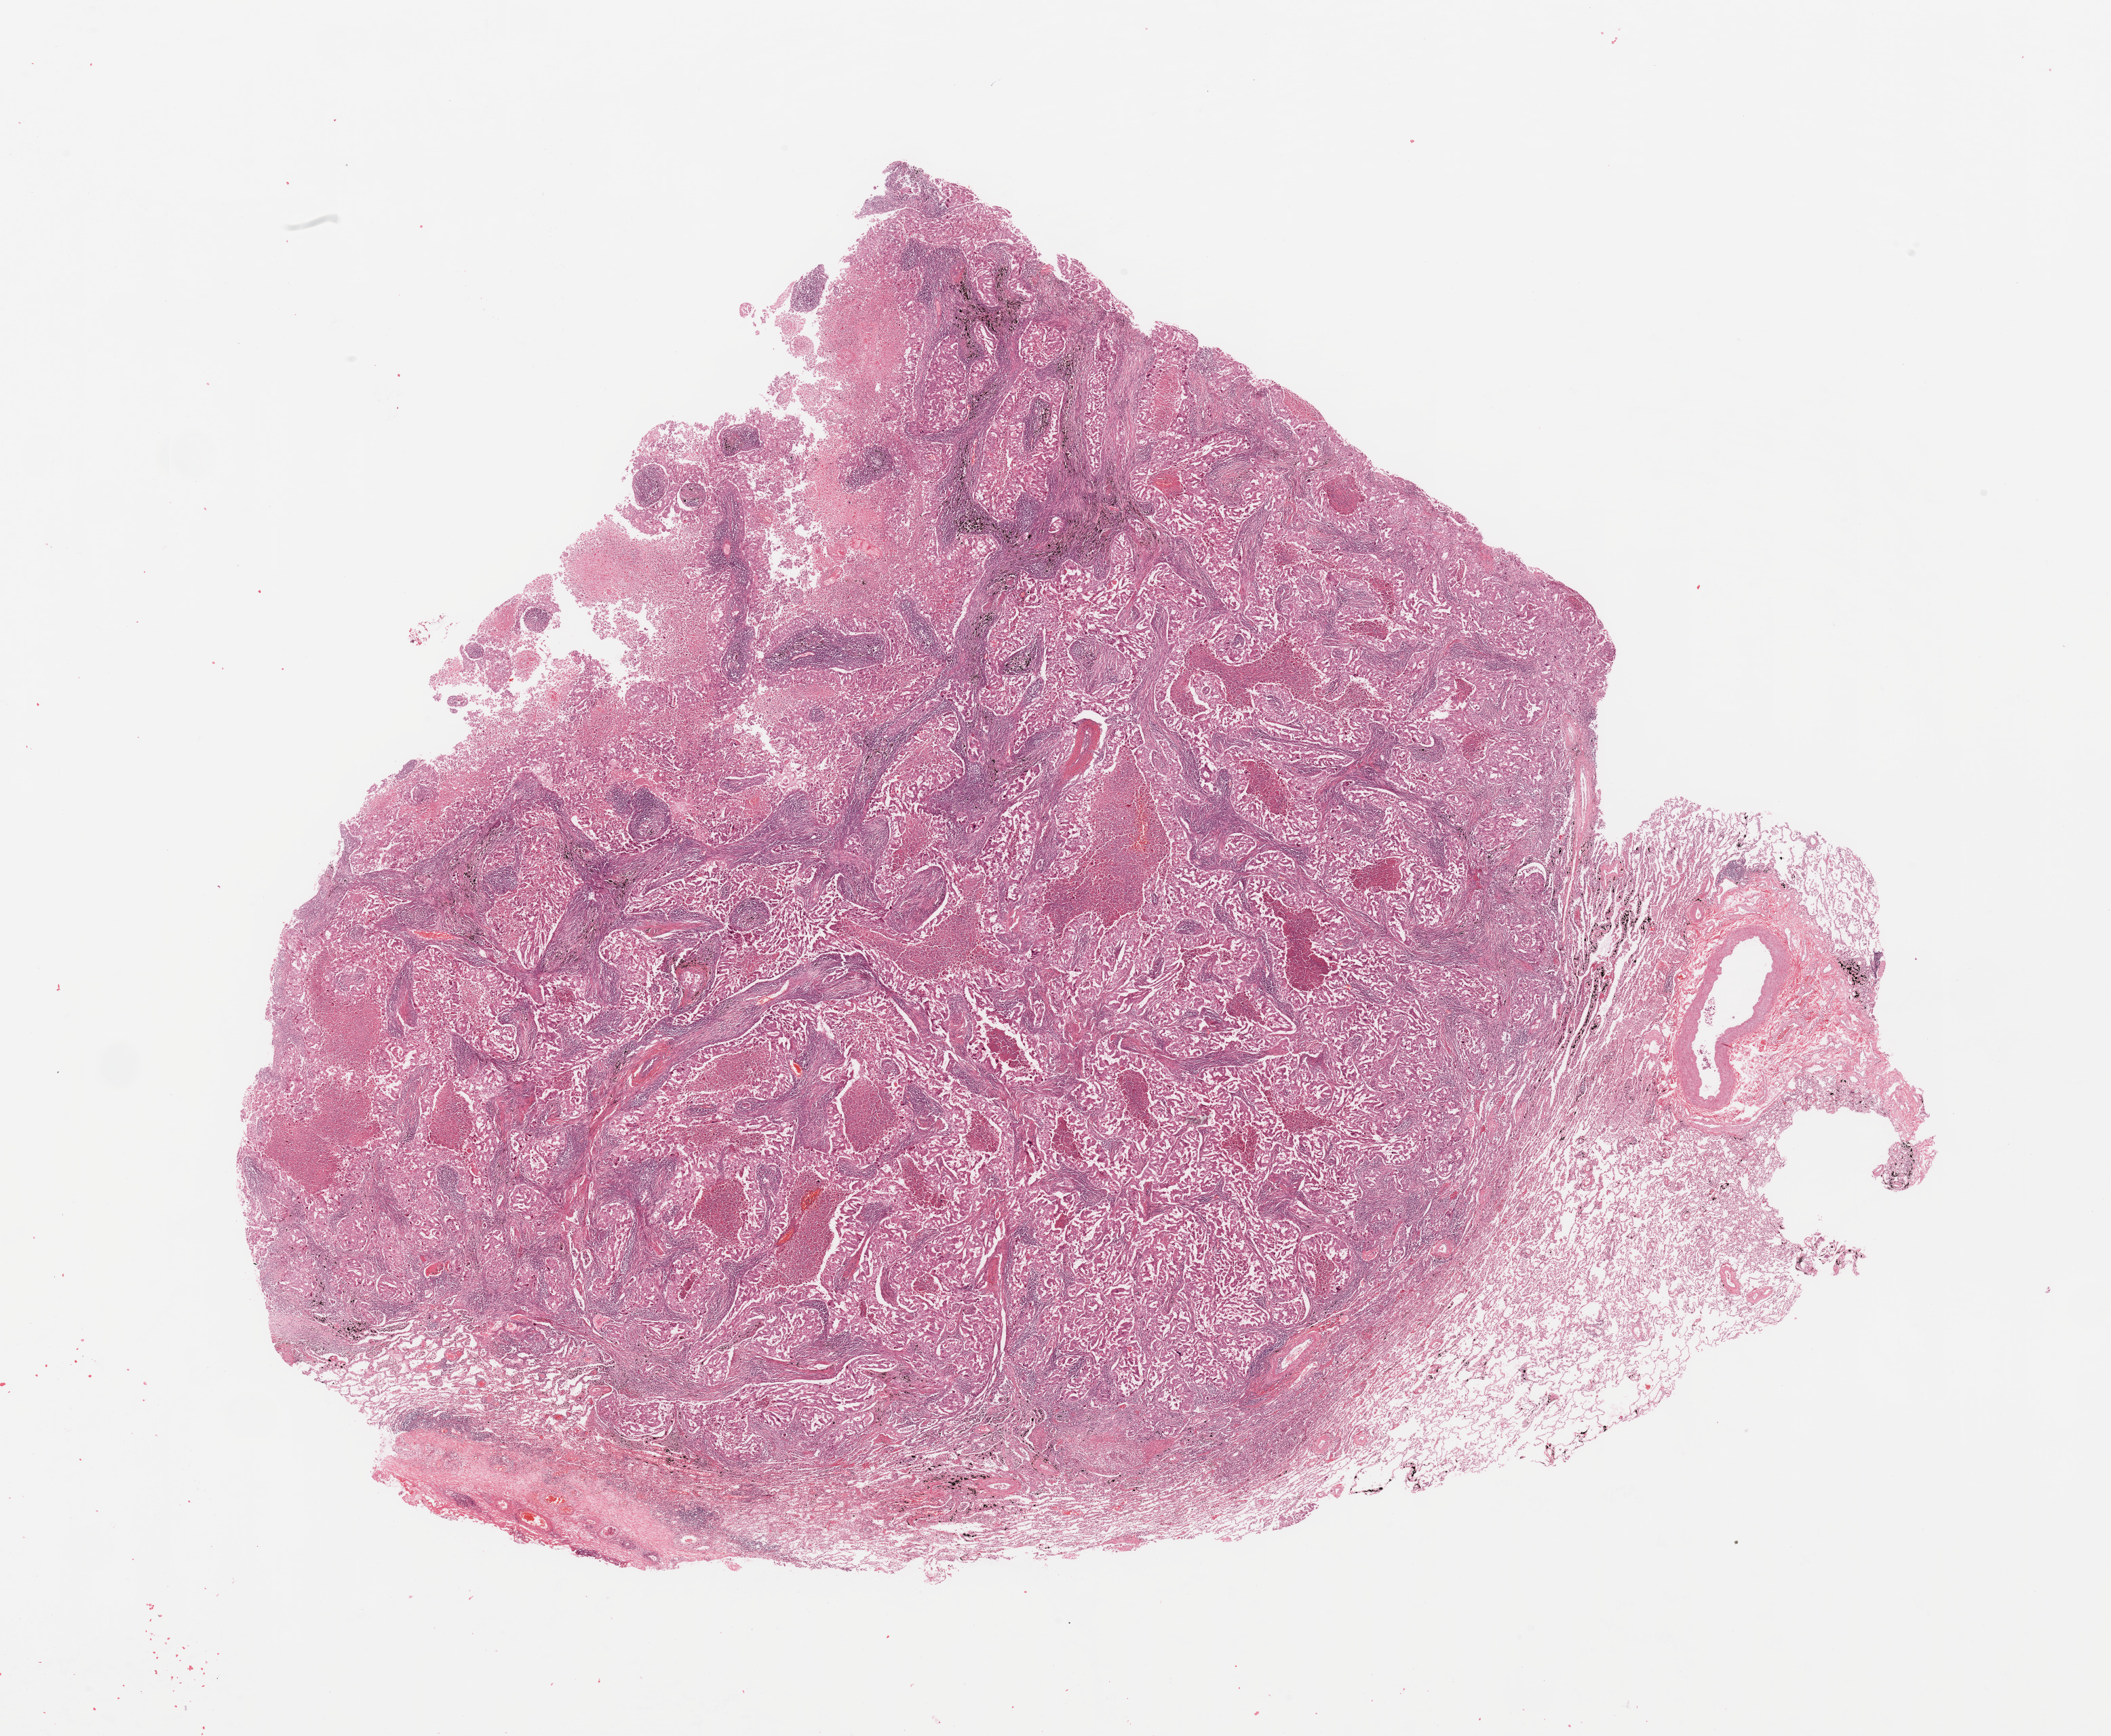
Whole-slide histology image, H&E-stained — a low-resolution overview of the entire scanned area, about 24.6 x 20.2 mm, tumour tissue sample, lung. Patient: male, age 54 years. Histologic grade: G2 (moderately differentiated).
AJCC pathologic stage: IB. Diagnosis: Adenocarcinoma, NOS.